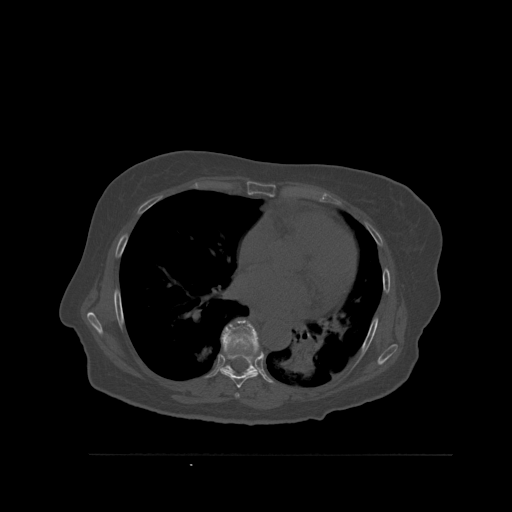
CT including the spine, one axial slice; slice 360 of 527 in the series (ordered by position); bone window (W 1800 / L 400 HU); 1.5 mm slice thickness; 512 × 512 image matrix, field of view 470 × 470 mm. Female patient, age 73 years. Case-level facts recorded for this patient, not image findings: primary cancer: breast; vertebrae with lytic lesions (as recorded): L2.
Annotated regions visible in this slice (semi-automatic segmentation, software-assisted and operator-edited):
- T6 vertebra: box from (x=235, y=393) to (x=240, y=398) px
- T7 vertebra: (x=220, y=351)–(x=261, y=388)
- T8 vertebra: (x=222, y=320)–(x=260, y=374)